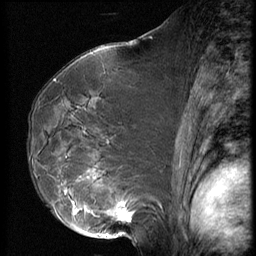
Breast MRI (dynamic contrast-enhanced), one sagittal slice. Slice 38 of 62 in the series (ordered by position). 3 images stored at this slice position (order not interpretable as contrast timing). 1.5 T. TE 4.2 ms, TR 9 ms. 2.5 mm slice thickness. 256 × 256 image matrix, field of view 180 × 180 mm. Patient: female, 50 years. From the clinical record (not read from this slice): setting: breast cancer imaged before/during neoadjuvant chemotherapy; receptor status: HR-positive, HER2-negative.
Outlined on this slice (semi-automatically segmented with operator editing):
- analysis volume of interest (the breast-tissue region the enhancement analysis was run in; not a lesion): box from (x=59, y=125) to (x=139, y=238) px
- tumour enhancement mask (voxels above the 140 % enhancement threshold inside the analysis volume of interest): (x=66, y=190)–(x=134, y=221)